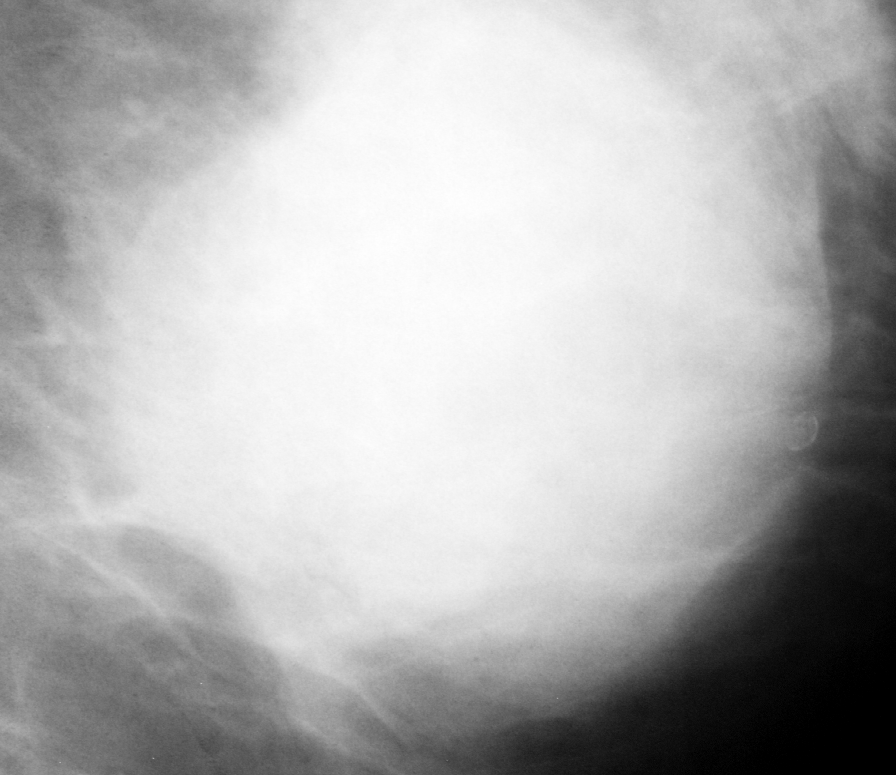
Cropped region of a digitized screen-film mammogram centred on a radiologist-marked abnormality, left breast, MLO view.
Mass, shape round, margins obscured; BI-RADS assessment category 4; pathology result (as recorded, not read from the image): benign.